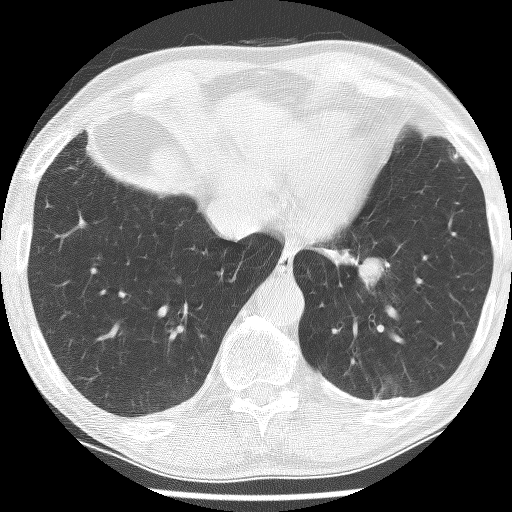
Low-dose screening chest CT, one axial slice; slice 40 of 226 in the series (ordered by position); reconstruction kernel BONE; 120 kVp; lung window (W 1500 / L -600 HU); 2.5 mm slice thickness; 512 × 512 image matrix.
Structures marked on this image (expert manual segmentation):
- lesion 1 (tumor, lower lobe of left lung): bounding box <341,252,384,290> (left, top, right, bottom; pixels)